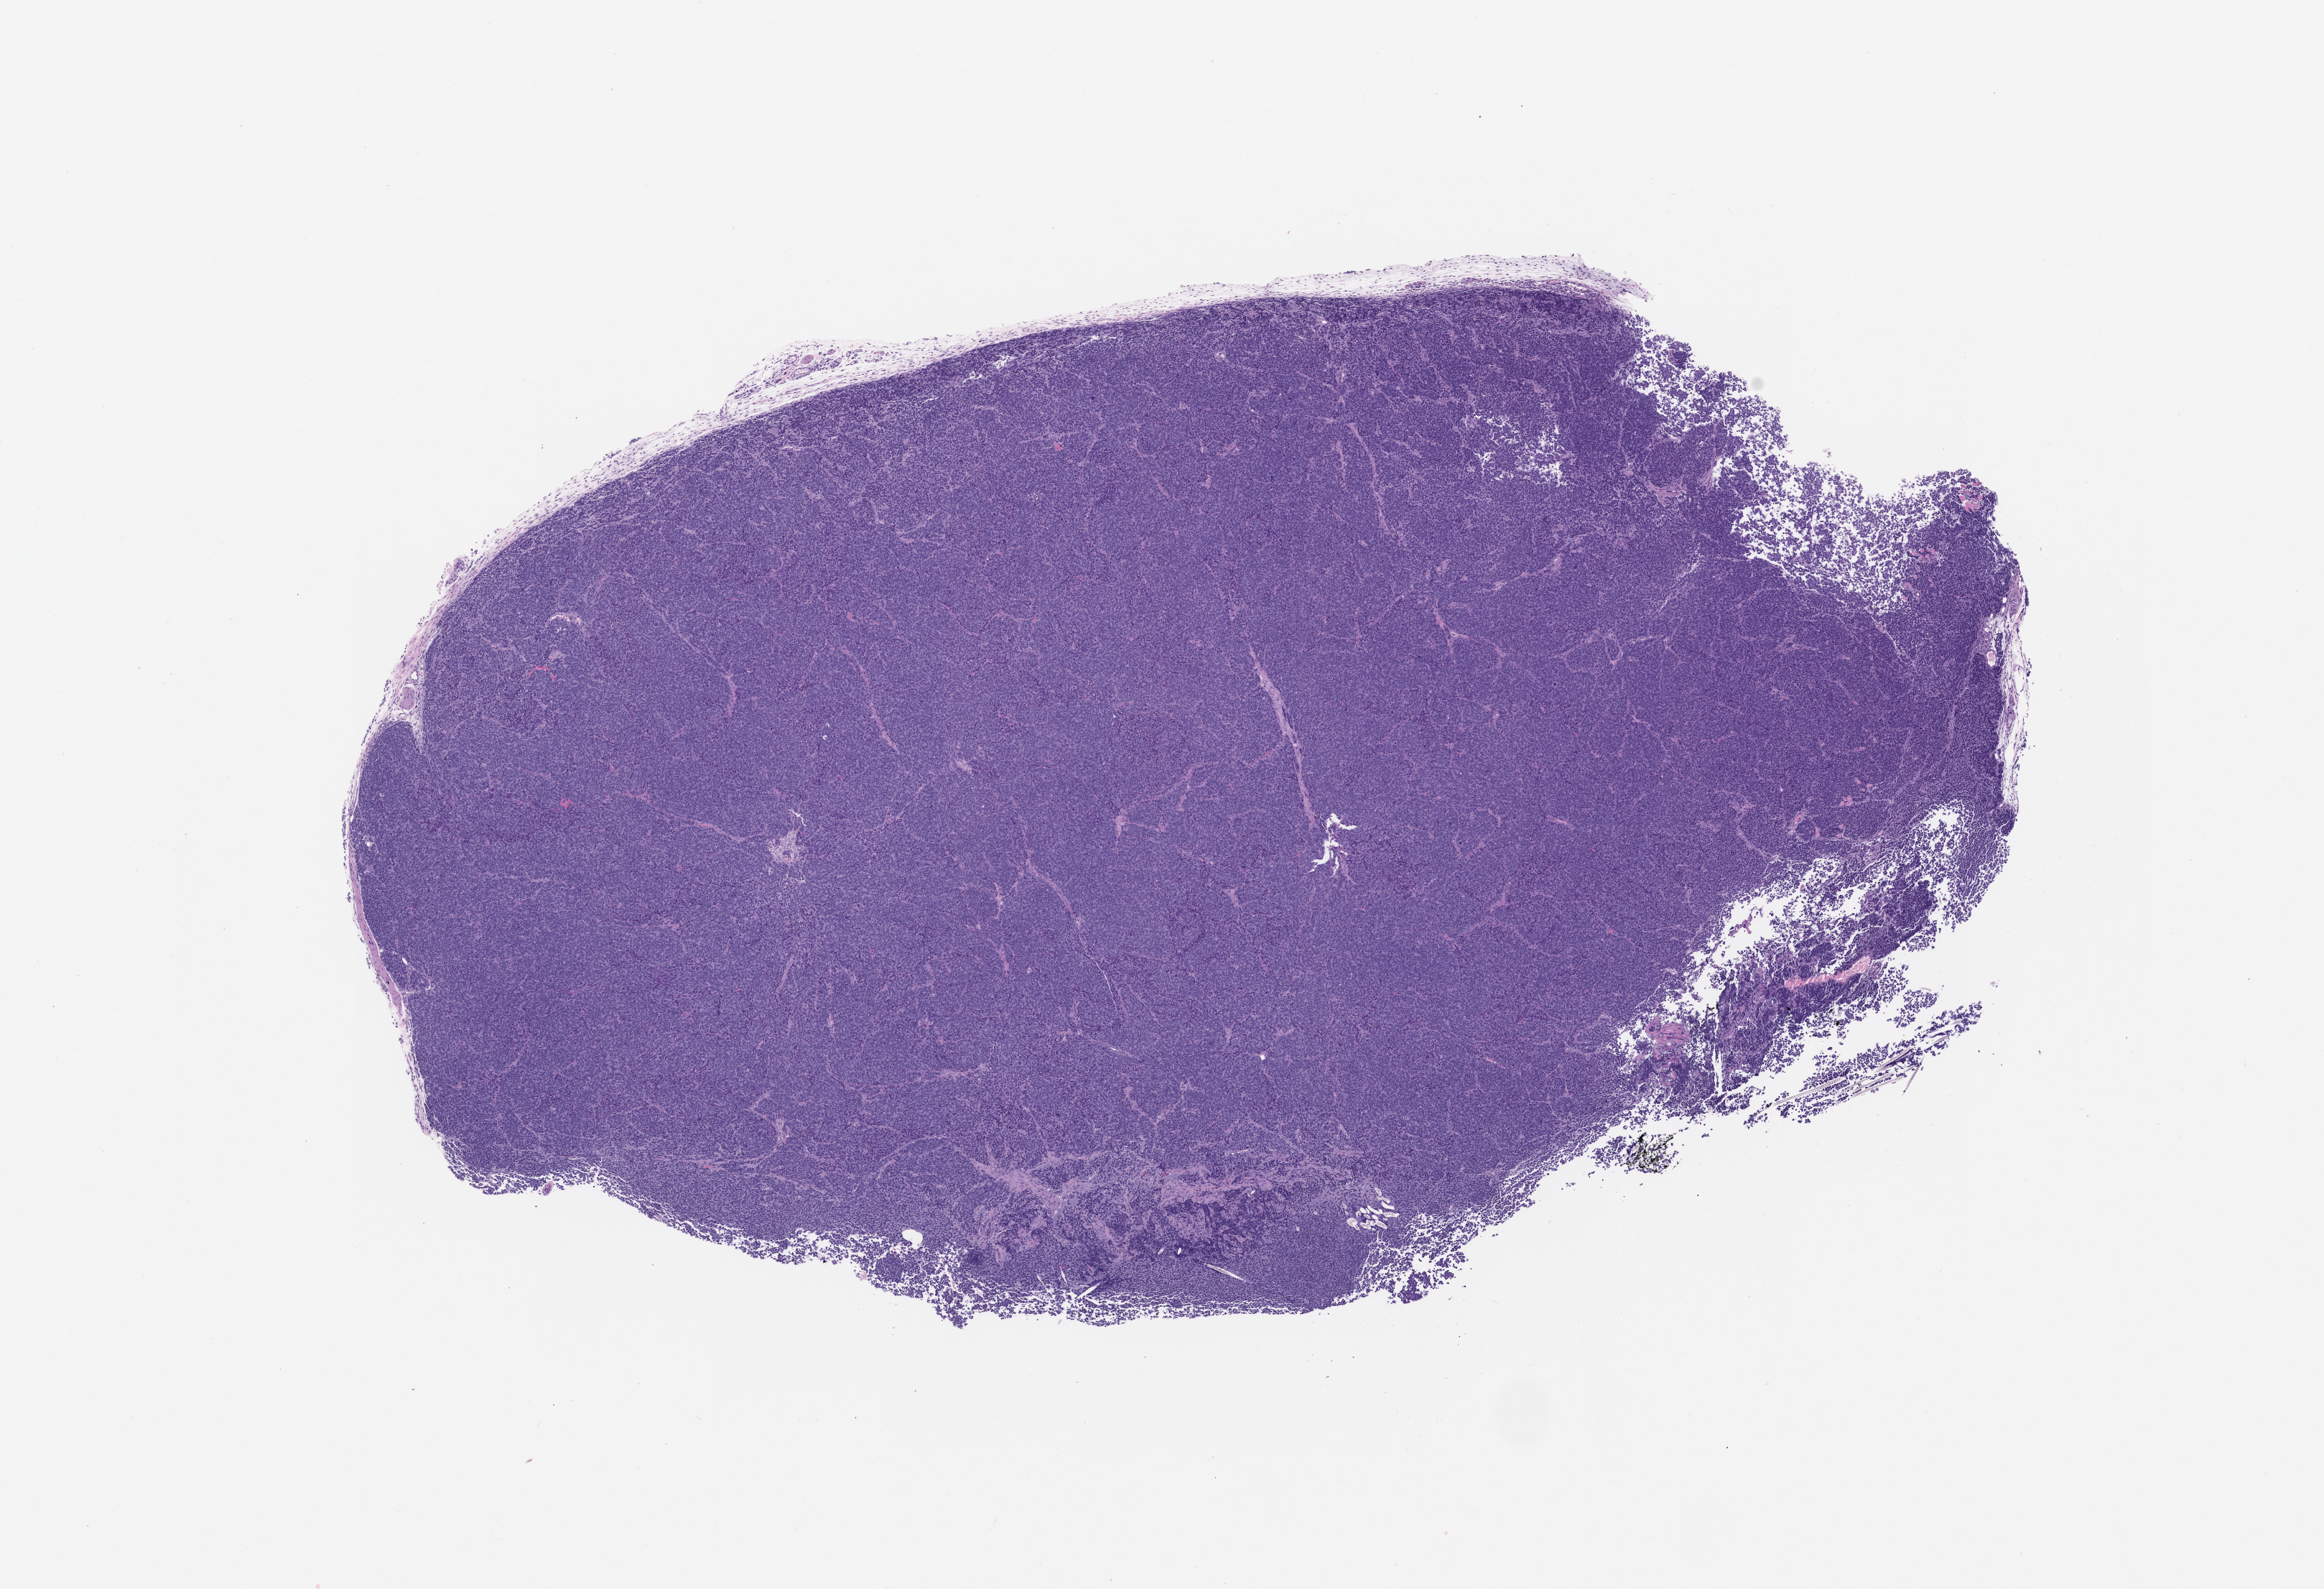
Haematoxylin and eosin whole-slide image of a patient-derived xenograft (PDX) tumor grown in a mouse, passage 1 — whole scanned area (about 13.0 x 8.9 mm) shown as a low-resolution overview, FFPE section, tumor site category: bladder.
• originating patient diagnosis: Bladder Small Cell Neuroendocrine Carcinoma